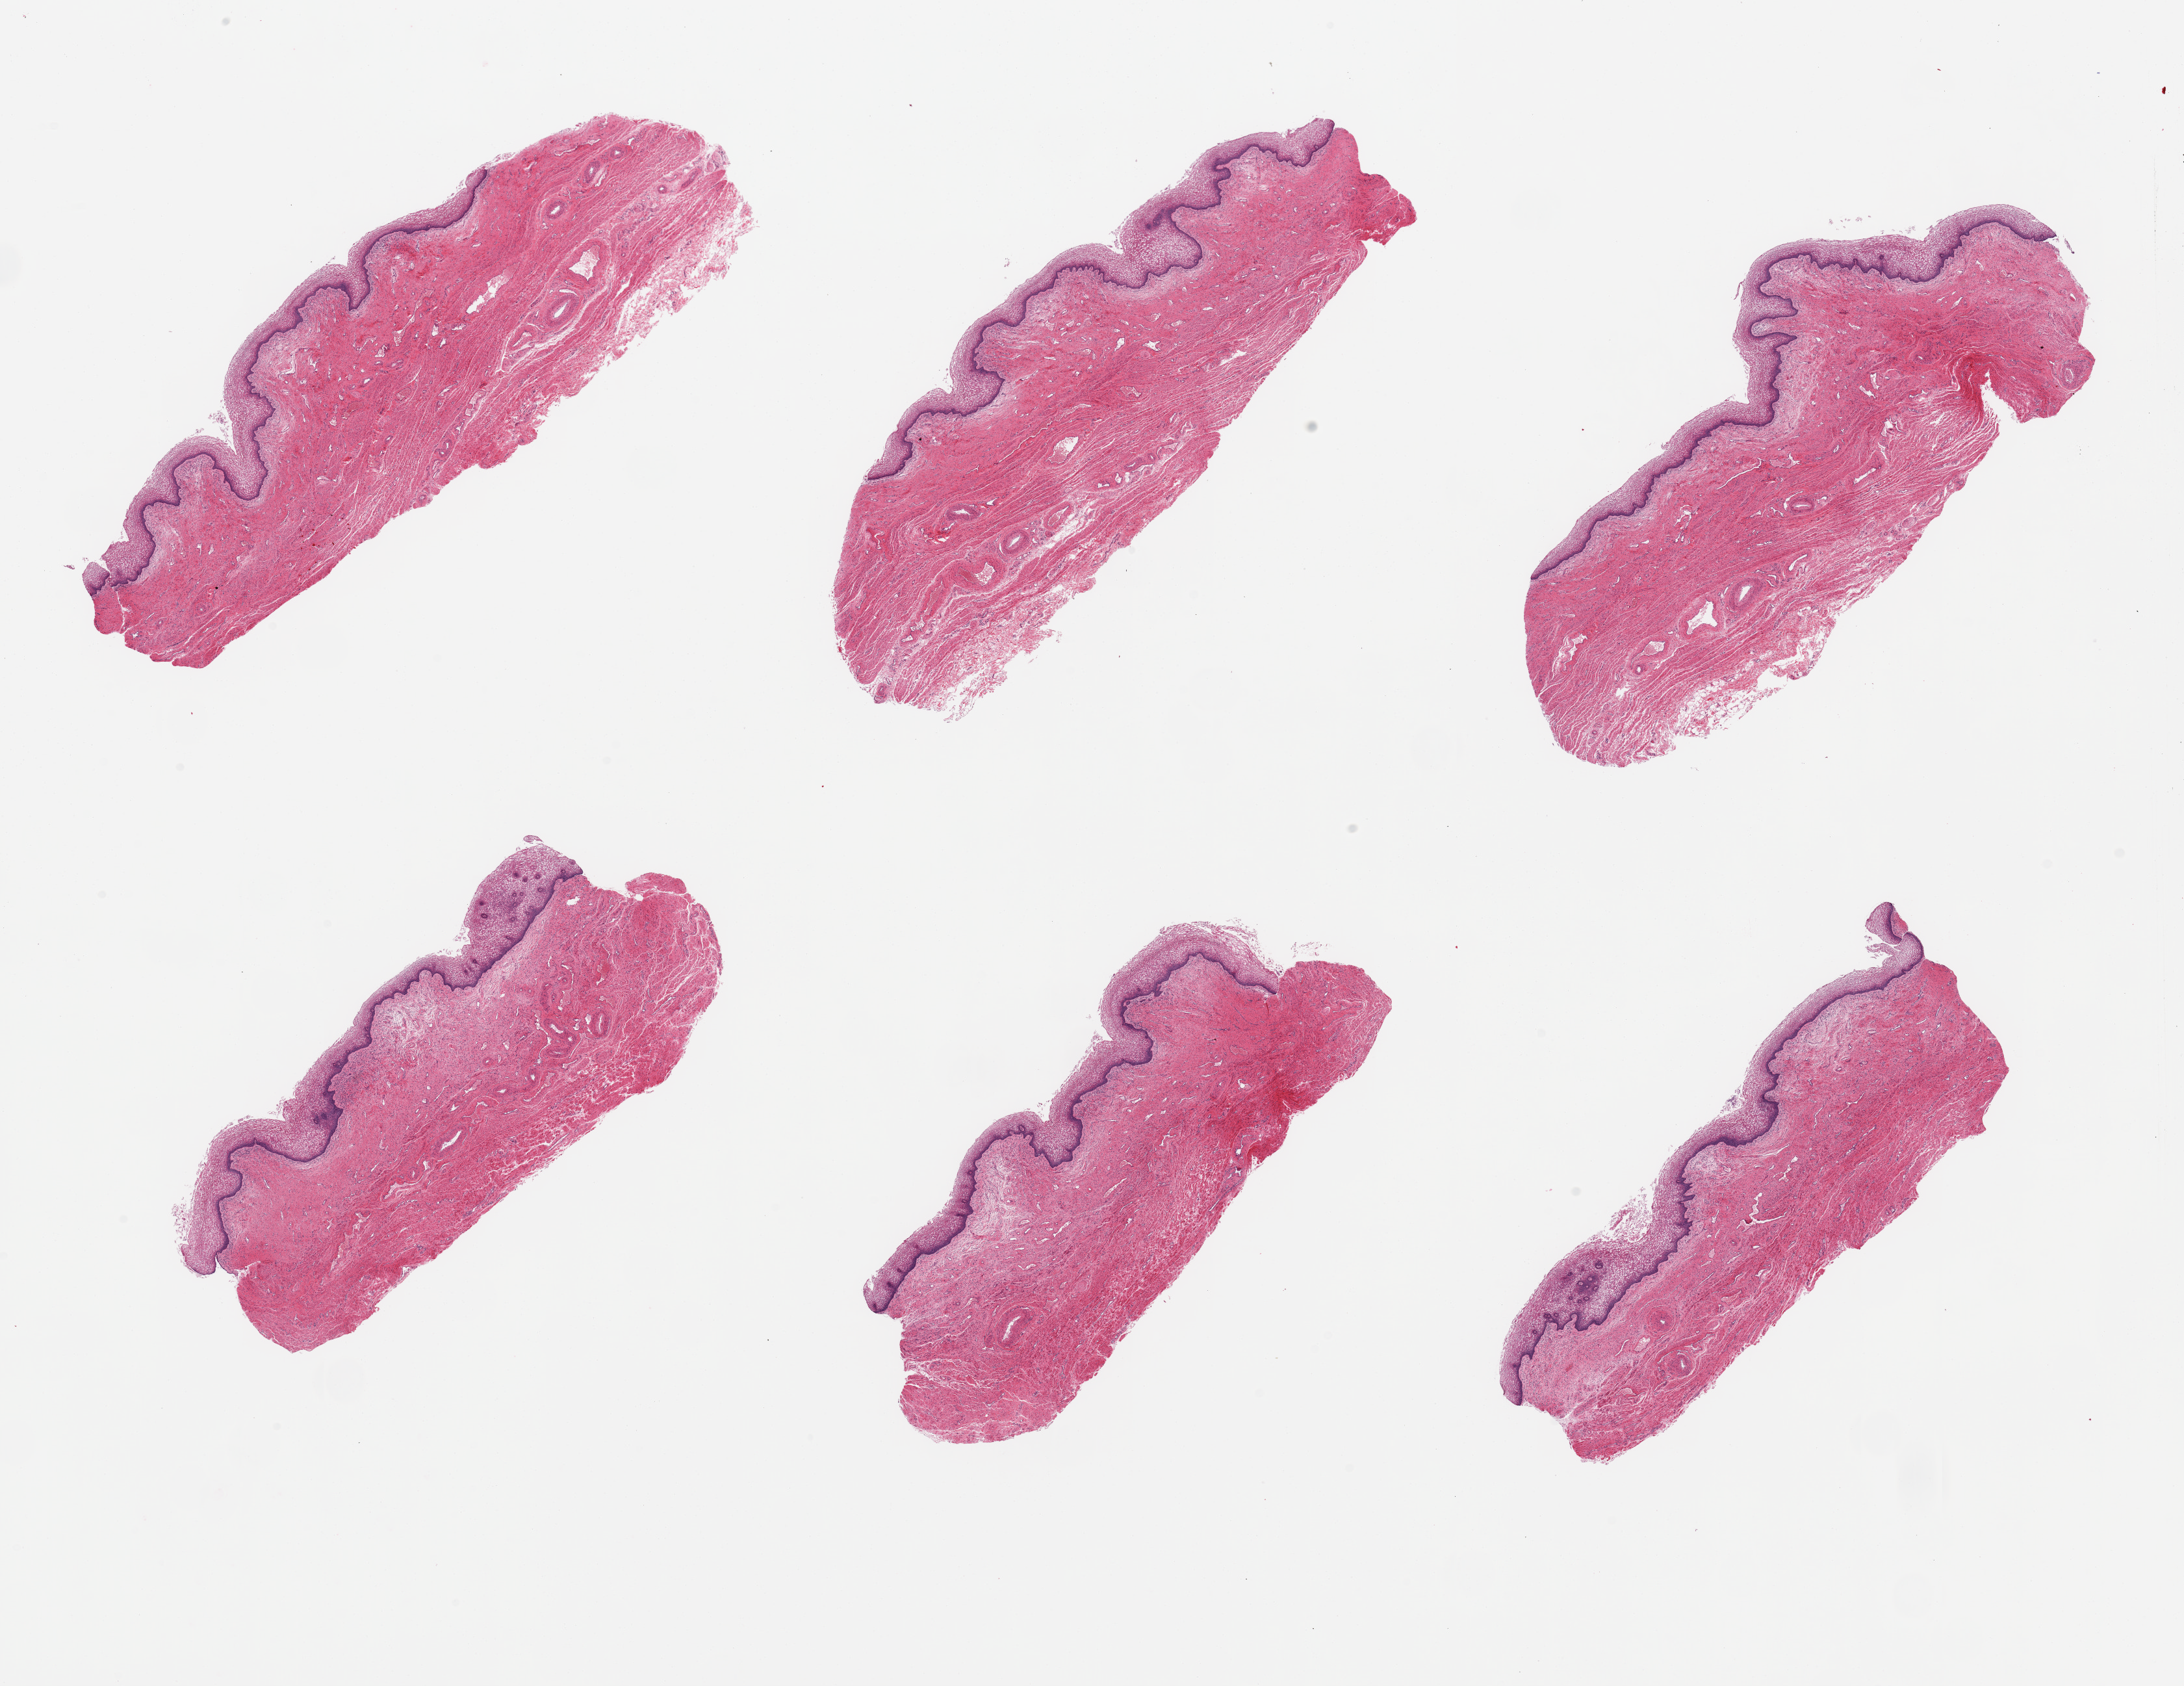
Digitized H&E-stained section, brightfield — shown as a low-resolution overview of the whole scanned area (about 26.6 x 20.5 mm, from a 20x scan). PAXgene-fixed paraffin-embedded (PFPE) section. Section of vagina (target tissue). Donor tissue sample. Donor: female.
Pathologist's review note for this sample: 6 pieces, well-glycogenated squamous mucosa up to ~0.2mm.